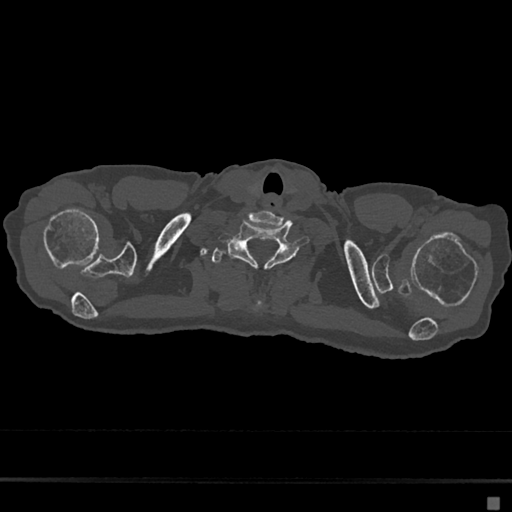
CT including the spine, one axial slice. Position 633 of 797 along the scan axis. 120 kVp. Bone window (W 1800 / L 400 HU). 512 × 512 image matrix, field of view 360 × 360 mm. Patient: female, 68 years. From the clinical record (not read from this slice): primary cancer: renal.
Annotated regions visible in this slice (semi-automatically segmented with operator editing):
- T1 vertebra: box from (x=211, y=247) to (x=264, y=309) px